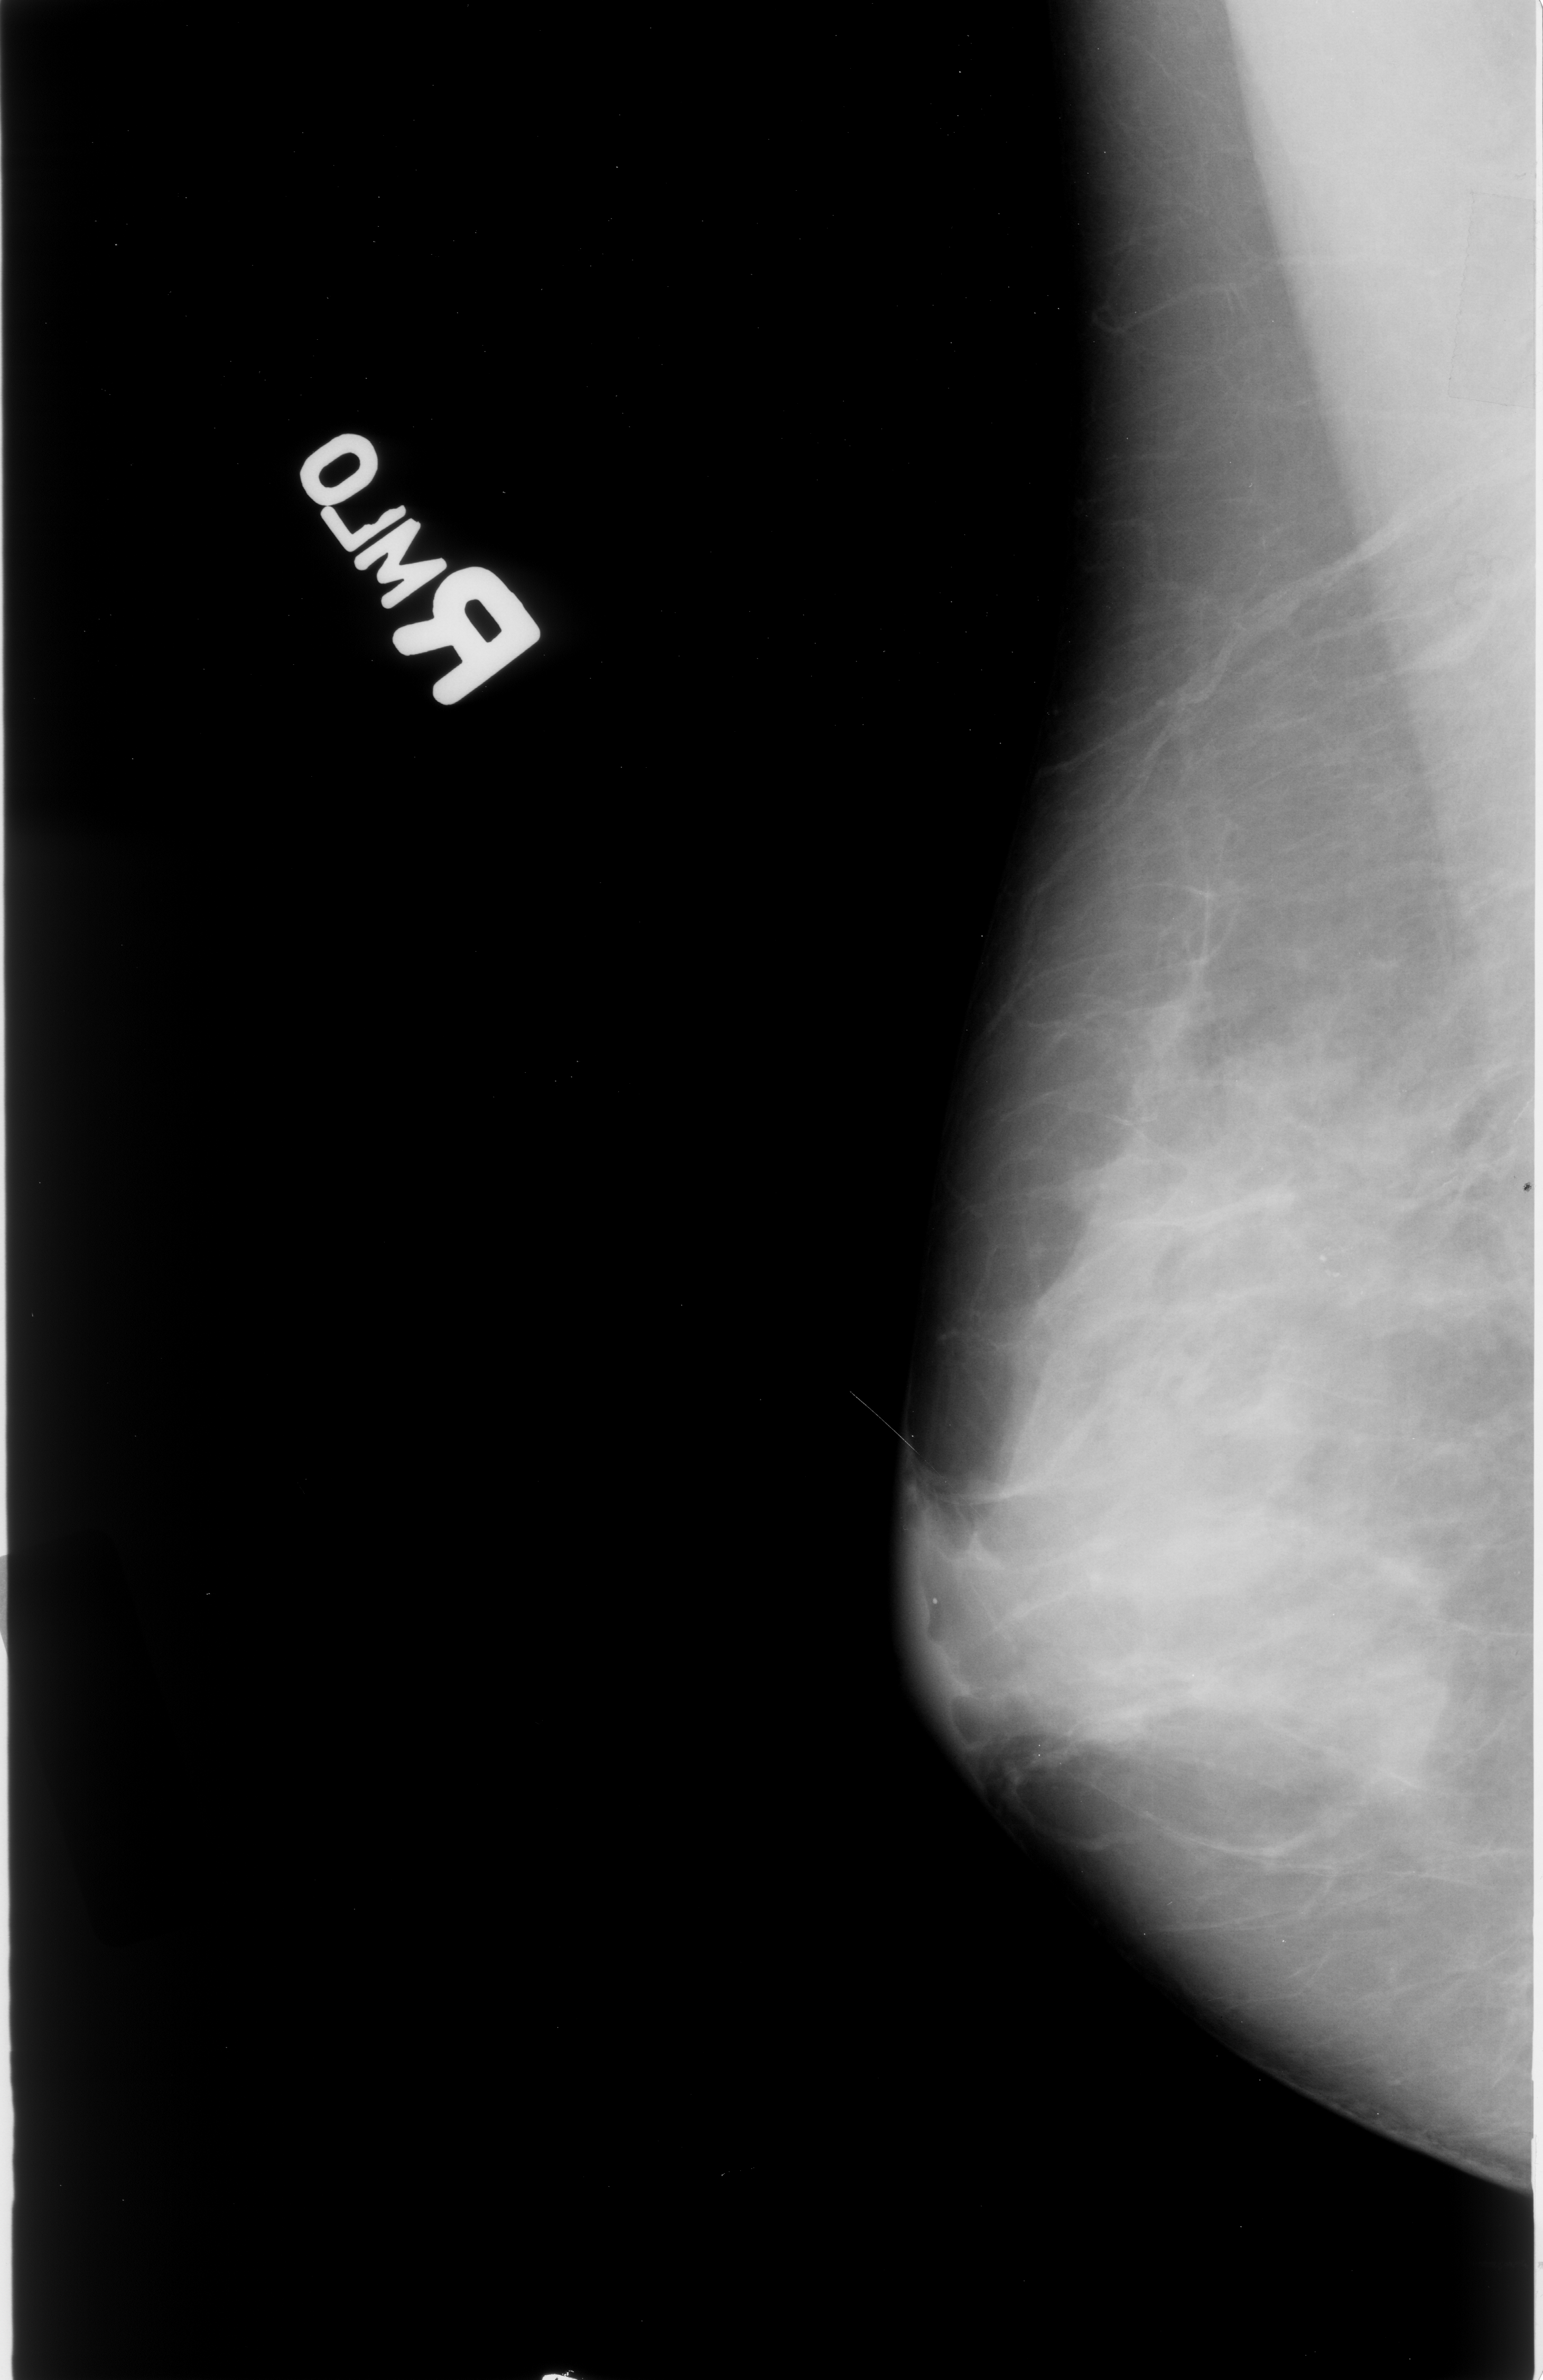
Digitized screen-film mammogram. Right breast. Mediolateral oblique (MLO) view. BI-RADS breast density category 3 (scale 1–4). 1543 × 2380 image matrix.
Marked abnormalities (boxes around the expert regions of interest):
- calcifications, morphology pleomorphic, distribution clustered; BI-RADS assessment category 4; pathology result (as recorded, not read from the image): malignant: bounding box [x1, y1, x2, y2] px = [1297, 1234, 1409, 1333]